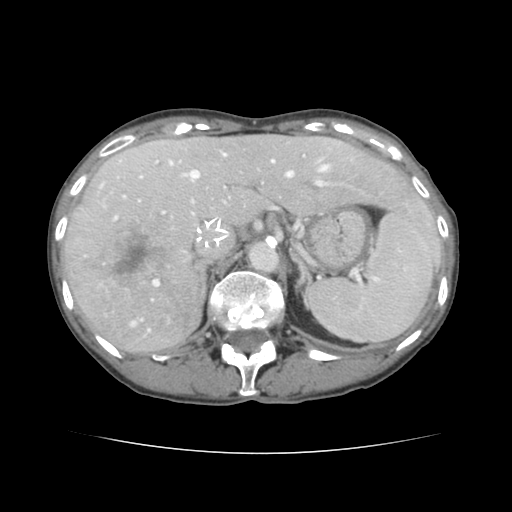
Contrast-enhanced abdominal CT, one axial slice. Slice 98 of 136 in the series (ordered by position). Intravenous contrast given. Soft-tissue window (W 400 / L 40 HU). 2.5 mm slice thickness. 512 × 512 image matrix. Female patient, age 77 years. From the clinical record (not read from this slice): diagnosis: colorectal cancer liver metastases, imaged before liver resection; multiple liver metastases: yes; largest metastasis: 3 cm; disease in both lobes: no.
Structures marked on this image (manually delineated by an expert):
- hepatic veins: bounding box <131,153,328,331> (left, top, right, bottom; pixels)
- liver: <65,136,441,353>
- planned liver remnant (the part of the liver to remain after resection): <156,136,440,252>
- portal vein (with intrahepatic branches): <114,173,364,286>
- liver metastasis: <86,220,176,297>